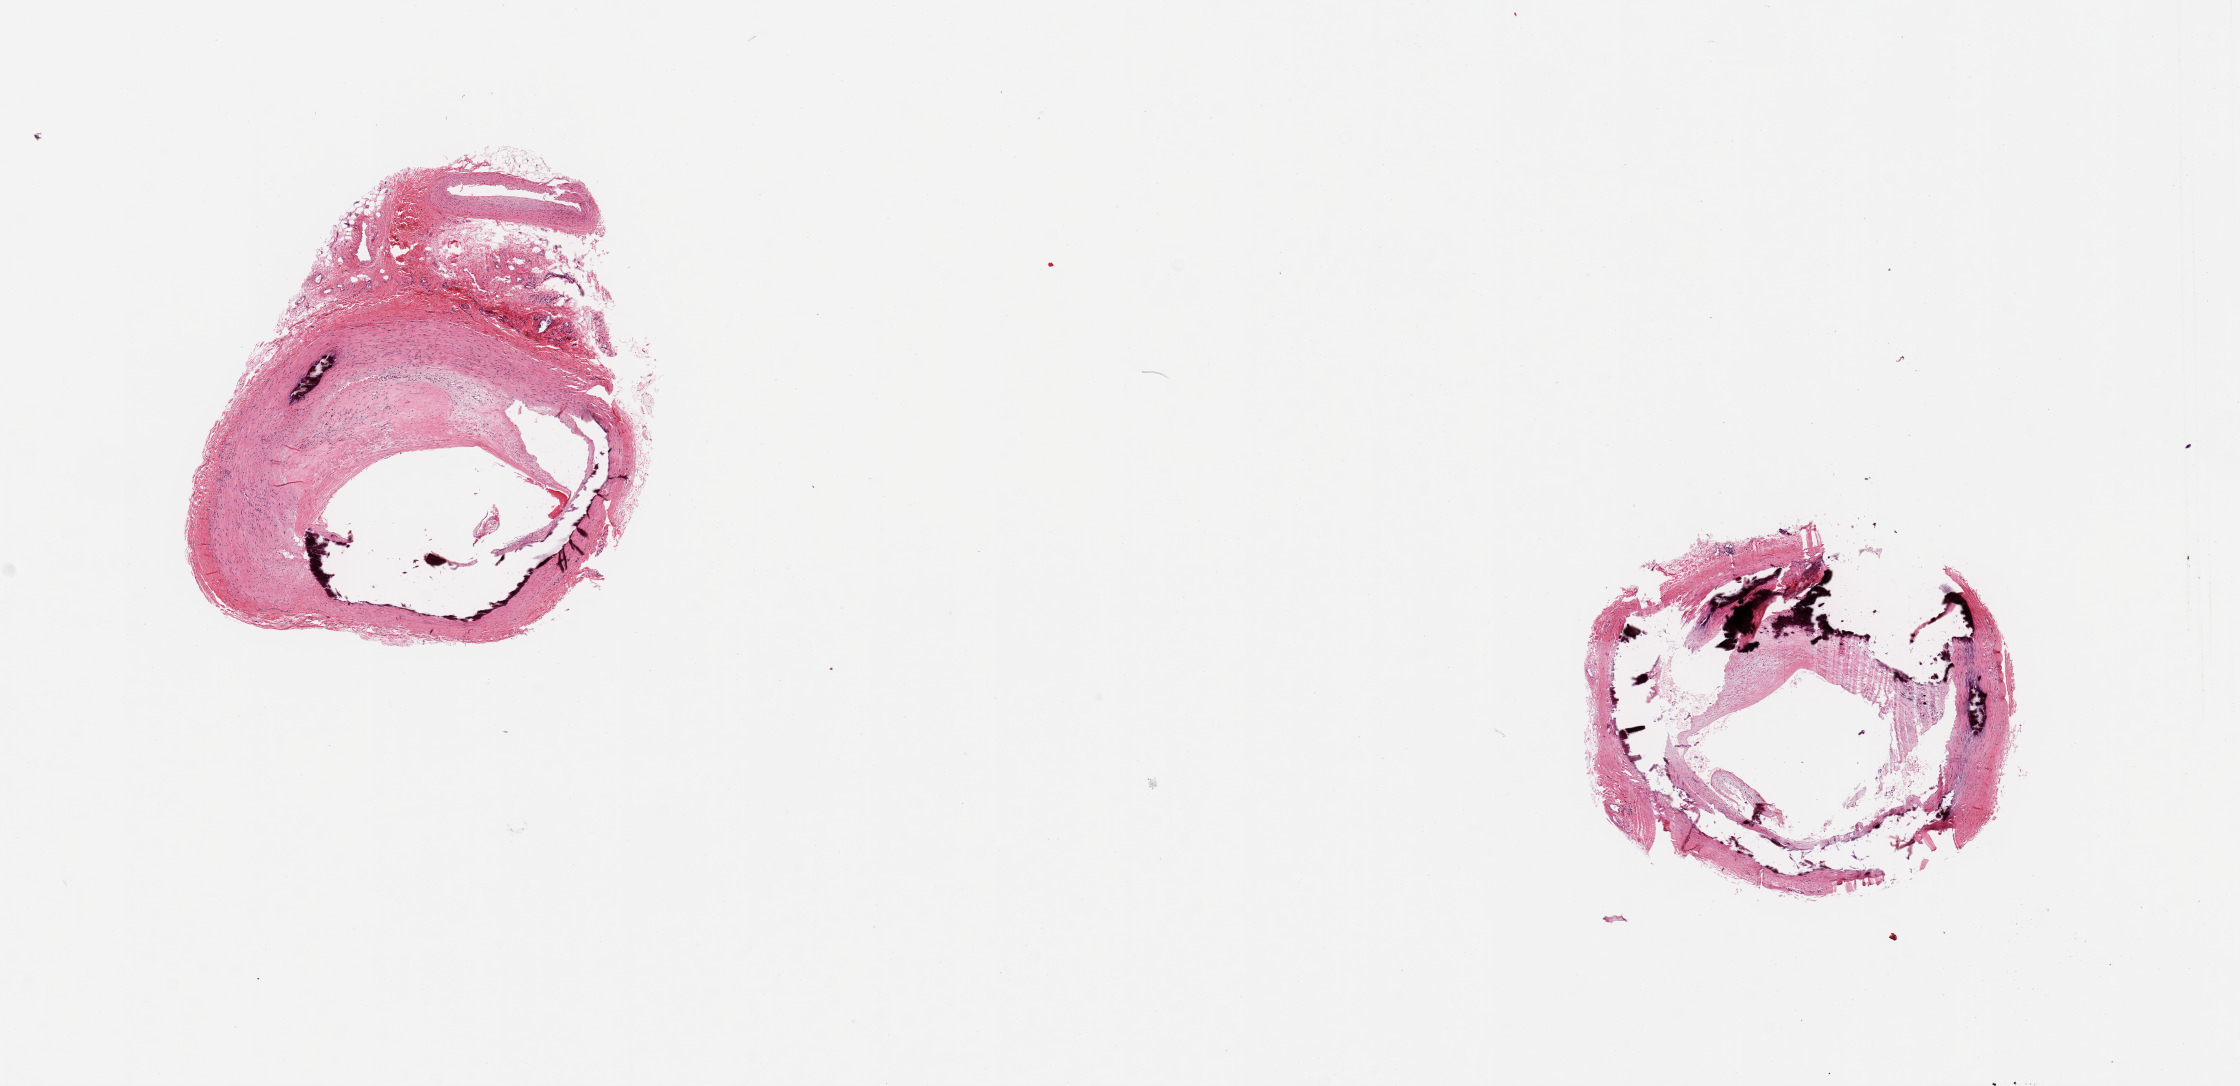
Haematoxylin and eosin whole-slide image, whole scanned area (about 17.7 x 8.6 mm) shown as a low-resolution overview, PAXgene-fixed, paraffin-embedded tissue, target tissue: tibial artery, tissue donor sample. Male donor.
Review note (as recorded): 2 pieces subtotally occlusive calcifying atherosis; ~!mm nubbin of adherent fibroadipose tissue.